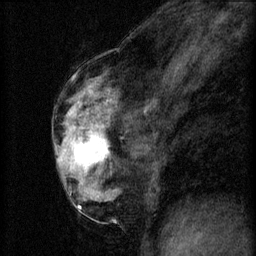
Breast MRI (dynamic contrast-enhanced), one sagittal slice. Slice 32 of 60 in the series (ordered by position). 3 images stored at this slice position (order not interpretable as contrast timing). 1.5 T. TE 4.2 ms, TR 8.2 ms. 2 mm slice thickness. 256 × 256 image matrix, field of view 180 × 180 mm. Patient: female, 56 years.
Annotated regions visible in this slice (semi-automatic segmentation, software-assisted and operator-edited):
- analysis volume of interest (the breast-tissue region the enhancement analysis was run in; not a lesion): bounding box (x1, y1, x2, y2) in pixels: (60, 124, 110, 179)
- tumour enhancement mask (voxels above the 70 % enhancement threshold inside the analysis volume of interest): (64, 126, 108, 167)